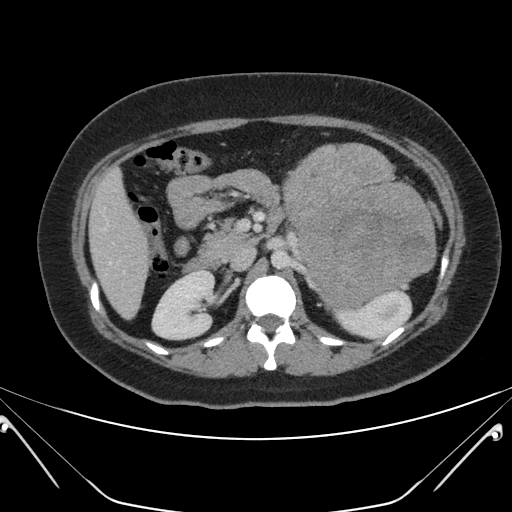
Contrast-enhanced abdominal CT, one axial slice. Position 115 of 168 along the scan axis. 120 kVp. Intravenous contrast given. Soft-tissue window (W 400 / L 40 HU). 3 mm slice thickness. 512 × 512 image matrix, field of view 394 × 394 mm. Female patient, age 26 years. From the clinical record (not read from this slice): diagnosis: adrenocortical carcinoma; tumour side: left adrenal; tumour size at pathology: 28 cm; Ki-67 index: 20 %; stage (as recorded): 2.
Structures marked on this image (semi-automatic segmentation, software-assisted and operator-edited):
- mass: bounding box <284,141,437,306> (left, top, right, bottom; pixels)